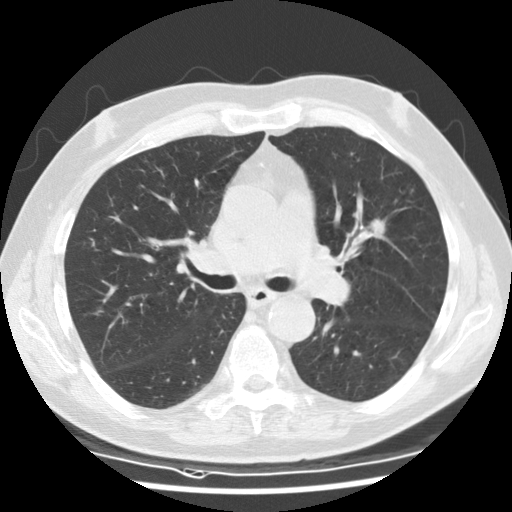
Chest CT (low-dose screening protocol), one axial image; first (baseline) screen; lung window (W 1500 / L -600 HU); 2.5 mm slice thickness; standard (soft-tissue) reconstruction kernel (STANDARD); 120 kVp; 512 × 512 image matrix, field of view 340 × 340 mm. Male, age 73 years at enrolment.
Lesion marked by an expert reader, box from (x=336, y=203) to (x=404, y=254) px. Screening reader's record for this exam (one nodule recorded; not confirmed to be the boxed lesion): non-calcified nodule or mass ≥4 mm, right lower lobe, 13 × 13 mm, smooth margins, soft tissue attenuation. Note: the box lies in the patient's left hemithorax on this image, whereas the reader's record names the right lung; they may be different findings. Official screen result: positive, change unspecified: nodule(s) >= 4 mm or enlarging nodule(s), mass(es), or other non-specific abnormalities suspicious for lung cancer.